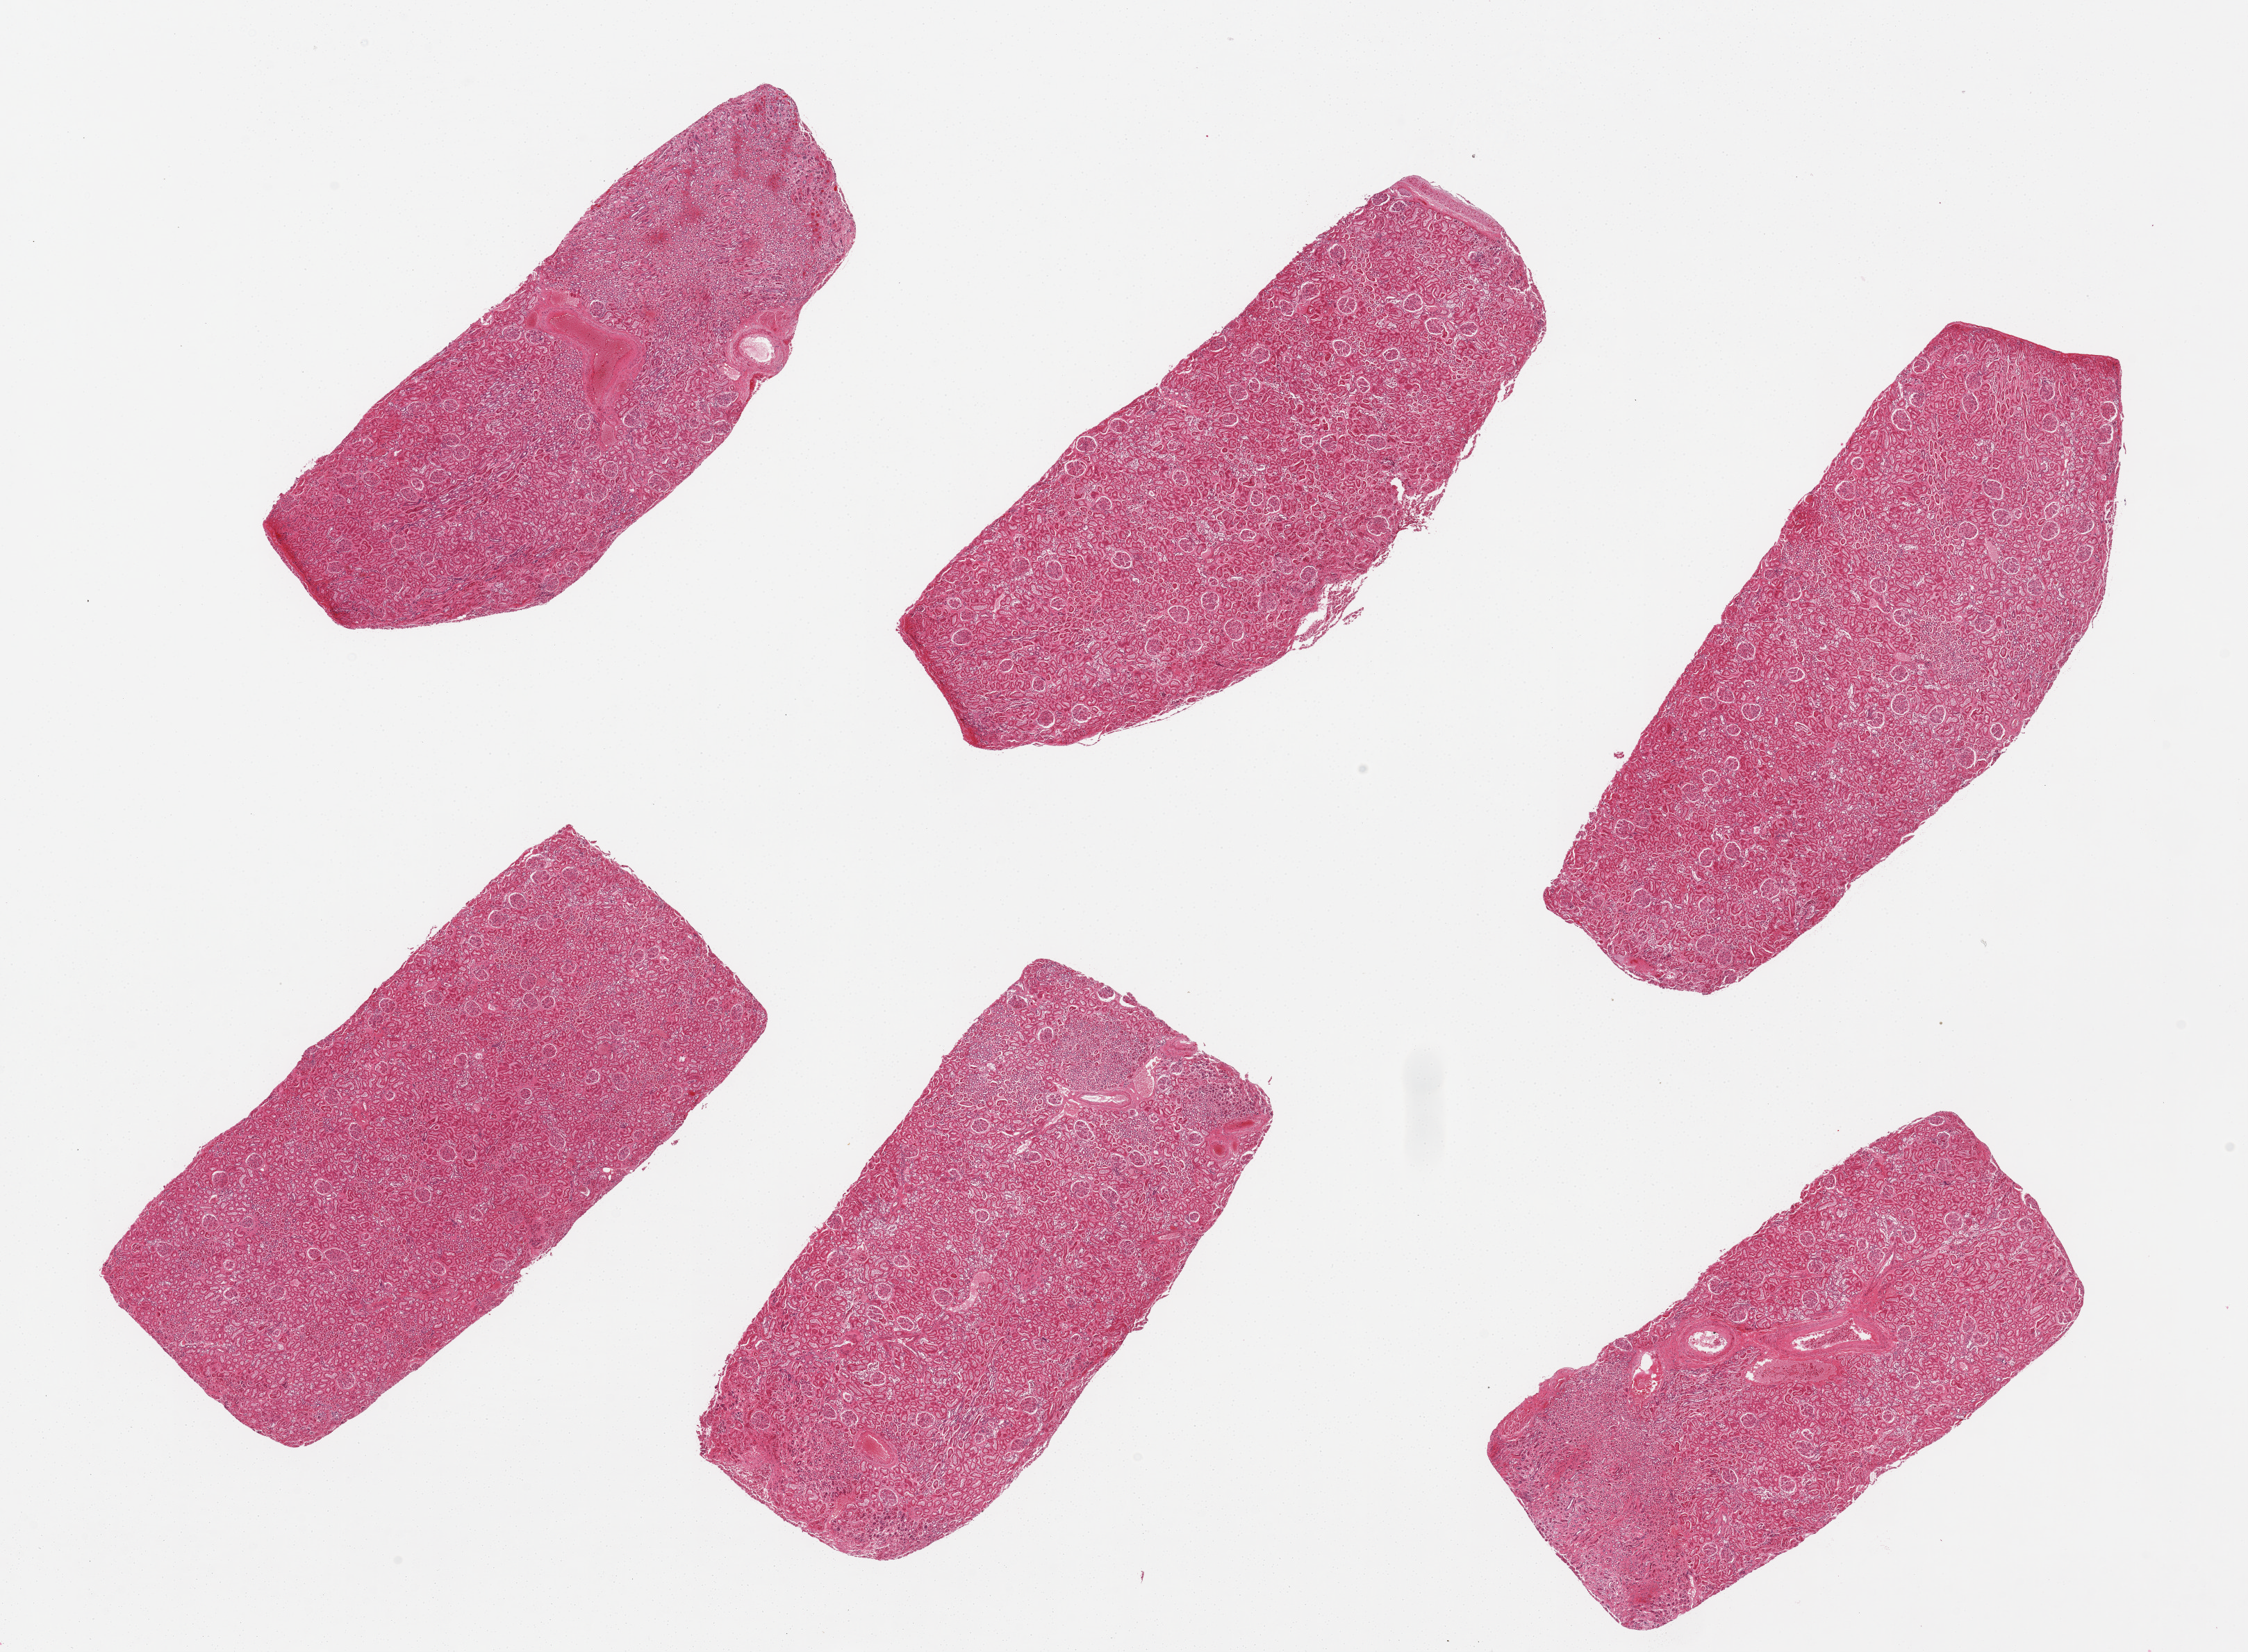
Whole-slide image, hematoxylin and eosin (H&E) stain, shown as a low-resolution overview of the whole scanned area (about 25.6 x 18.8 mm), PAXgene-fixed paraffin-embedded (PFPE) section, sampled site (target tissue): renal cortex, donor tissue sample. Donor: female.
Reviewer comment on this tissue sample: 6 pieces, all cortex; tubules moderately-severely autolzed.